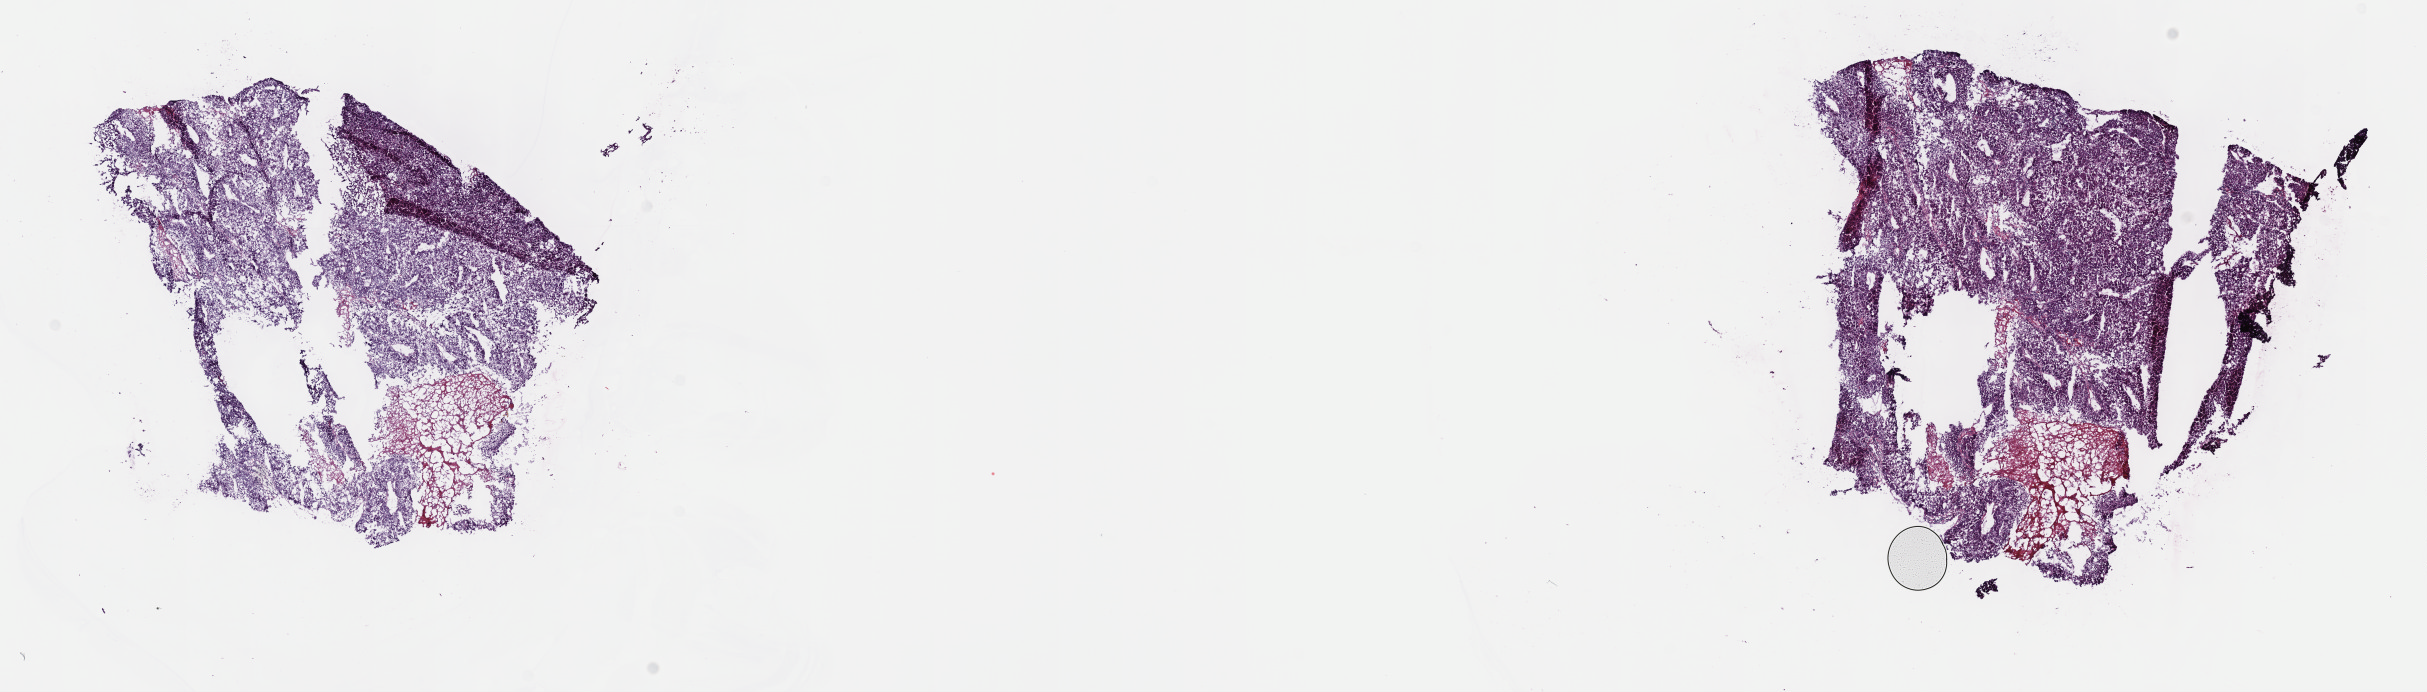
Whole-slide histology image, Hematoxylin and eosin (H&E) stained — a low-resolution overview of the entire scanned area, about 19.6 x 5.6 mm (slide scanned at 40x); frozen section from the top of the tissue portion; primary tumour sample from the liver. Male patient; age at initial diagnosis 68 years. Histologic grade: G2 (moderately differentiated). Slide review estimates, as recorded: tumour cells 89%, tumour nuclei 95%, normal cells 0%, stromal cells 8%, necrosis 3%. Inflammatory infiltration, as recorded: lymphocyte infiltration 6%, monocyte infiltration 1%, neutrophil infiltration 1%.
AJCC pathologic stage: IIIA (6th edition). Histologic diagnosis: Hepatocellular carcinoma, NOS.